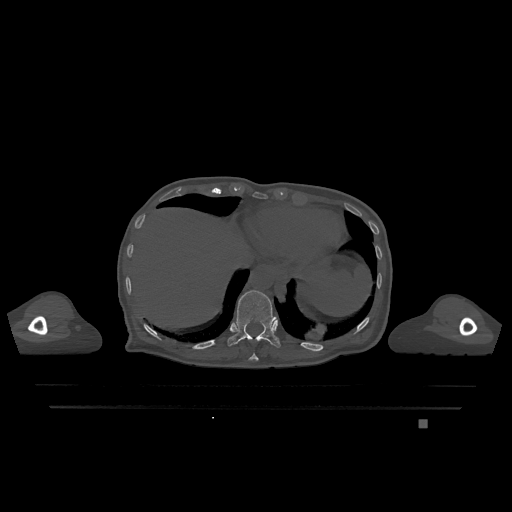
CT including the spine, one axial slice; slice 599 of 1317 in the series (ordered by position); bone window (W 1800 / L 400 HU); 0.5 mm slice thickness; 512 × 512 image matrix, field of view 500 × 500 mm. Patient: female, 74 years. Case-level facts recorded for this patient, not image findings: primary cancer: lung.
Outlined on this slice (semi-automatic segmentation, software-assisted and operator-edited):
- T10 vertebra: bounding box (x1, y1, x2, y2) in pixels: (249, 354, 259, 361)
- T11 vertebra: (228, 290, 281, 348)